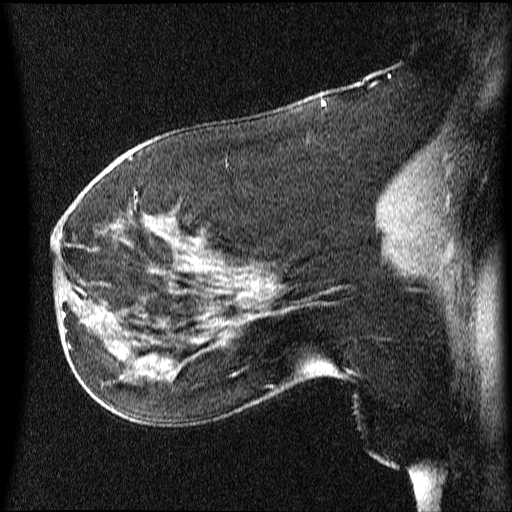
Breast MRI (dynamic contrast-enhanced), one sagittal slice; position 33 of 64 along the scan axis; dynamic contrast-enhanced series, image 2 of 4 at this slice position (ordered by acquisition); 1.5 T; TE 4.2 ms, TR 9 ms; 512 × 512 image matrix, field of view 200 × 200 mm. Female patient, age 63 years.
Outlined on this slice (semi-automatically segmented with operator editing):
- analysis volume of interest (the breast-tissue region the enhancement analysis was run in; not a lesion): box from (x=66, y=274) to (x=131, y=353) px
- tumour enhancement mask (voxels above the 70 % enhancement threshold inside the analysis volume of interest): (x=78, y=302)–(x=121, y=353)